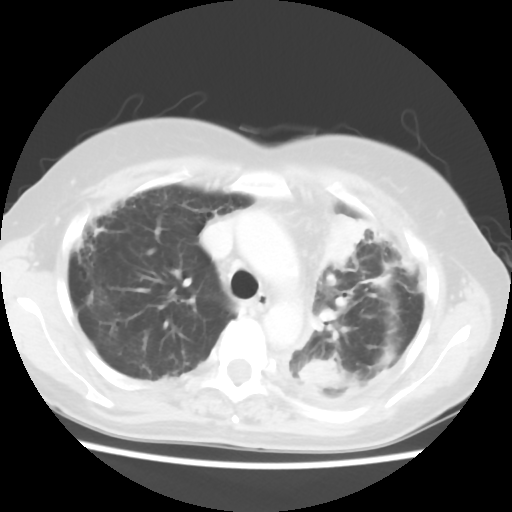
Chest CT, one axial slice; position 40 of 56 along the scan axis; 120 kVp; lung window (W 1500 / L -600 HU); 5 mm slice thickness; 512 × 512 image matrix, field of view 309 × 309 mm. Patient: female, 56 years. Case-level facts recorded for this patient, not image findings: clinical TNM (as recorded): T1c N0 M1.
Outlined on this slice (rectangle marked by the reading radiologist):
- lung tumour (recorded histology: adenocarcinoma): bounding box [x1, y1, x2, y2] px = [312, 204, 366, 273]